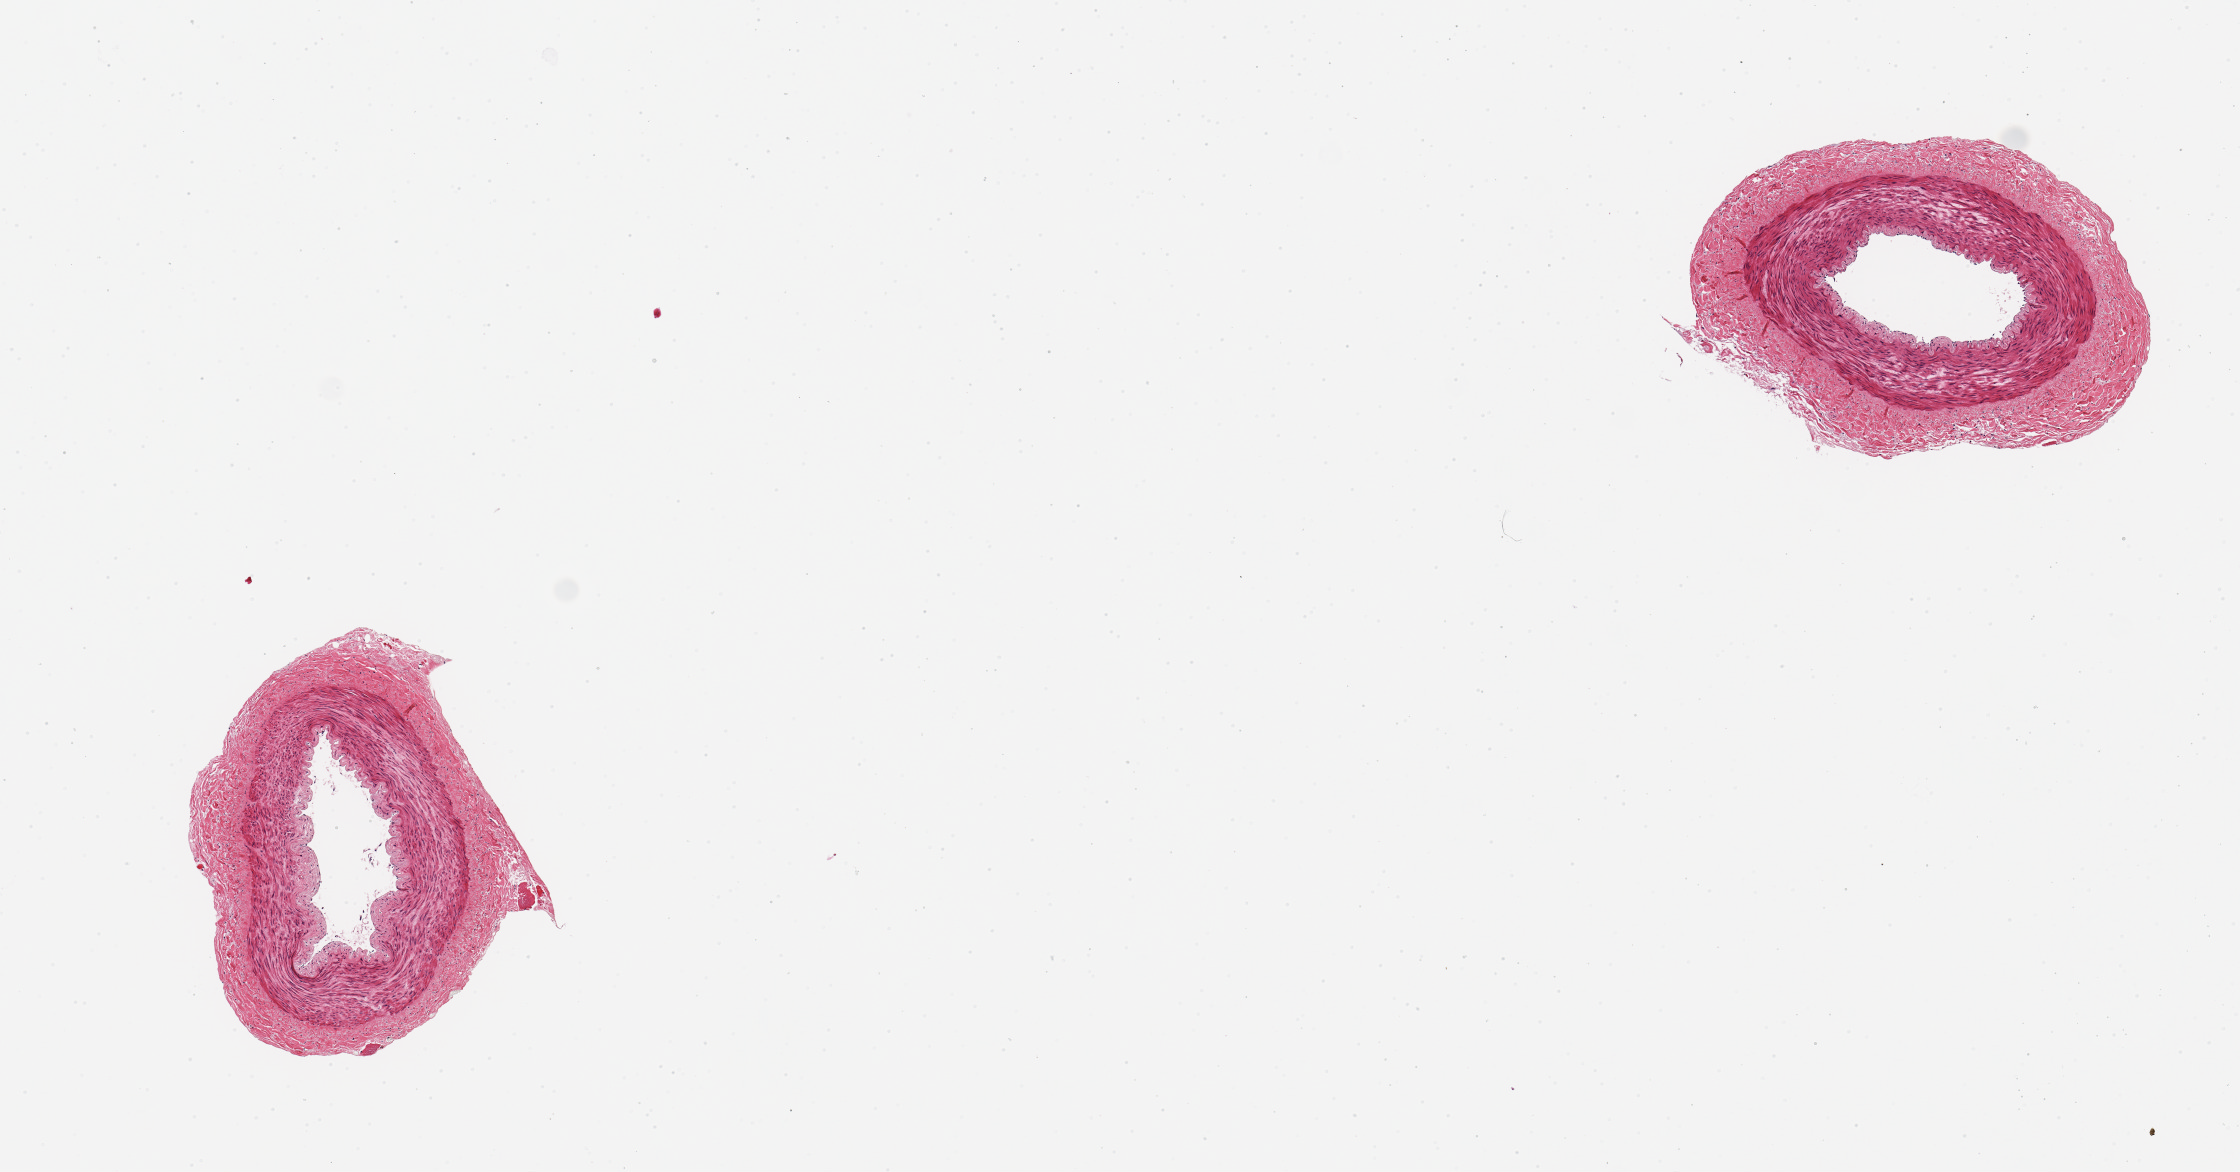
Digitized hematoxylin and eosin (H&E)-stained section, shown as a low-resolution overview of the whole scanned area (about 8.9 x 4.6 mm), PAXgene-fixed paraffin-embedded (PFPE) section, section of tibial artery (target tissue), donor tissue sample. Female donor.
- reviewer comment on this tissue sample: 2 pieces; well trimmed